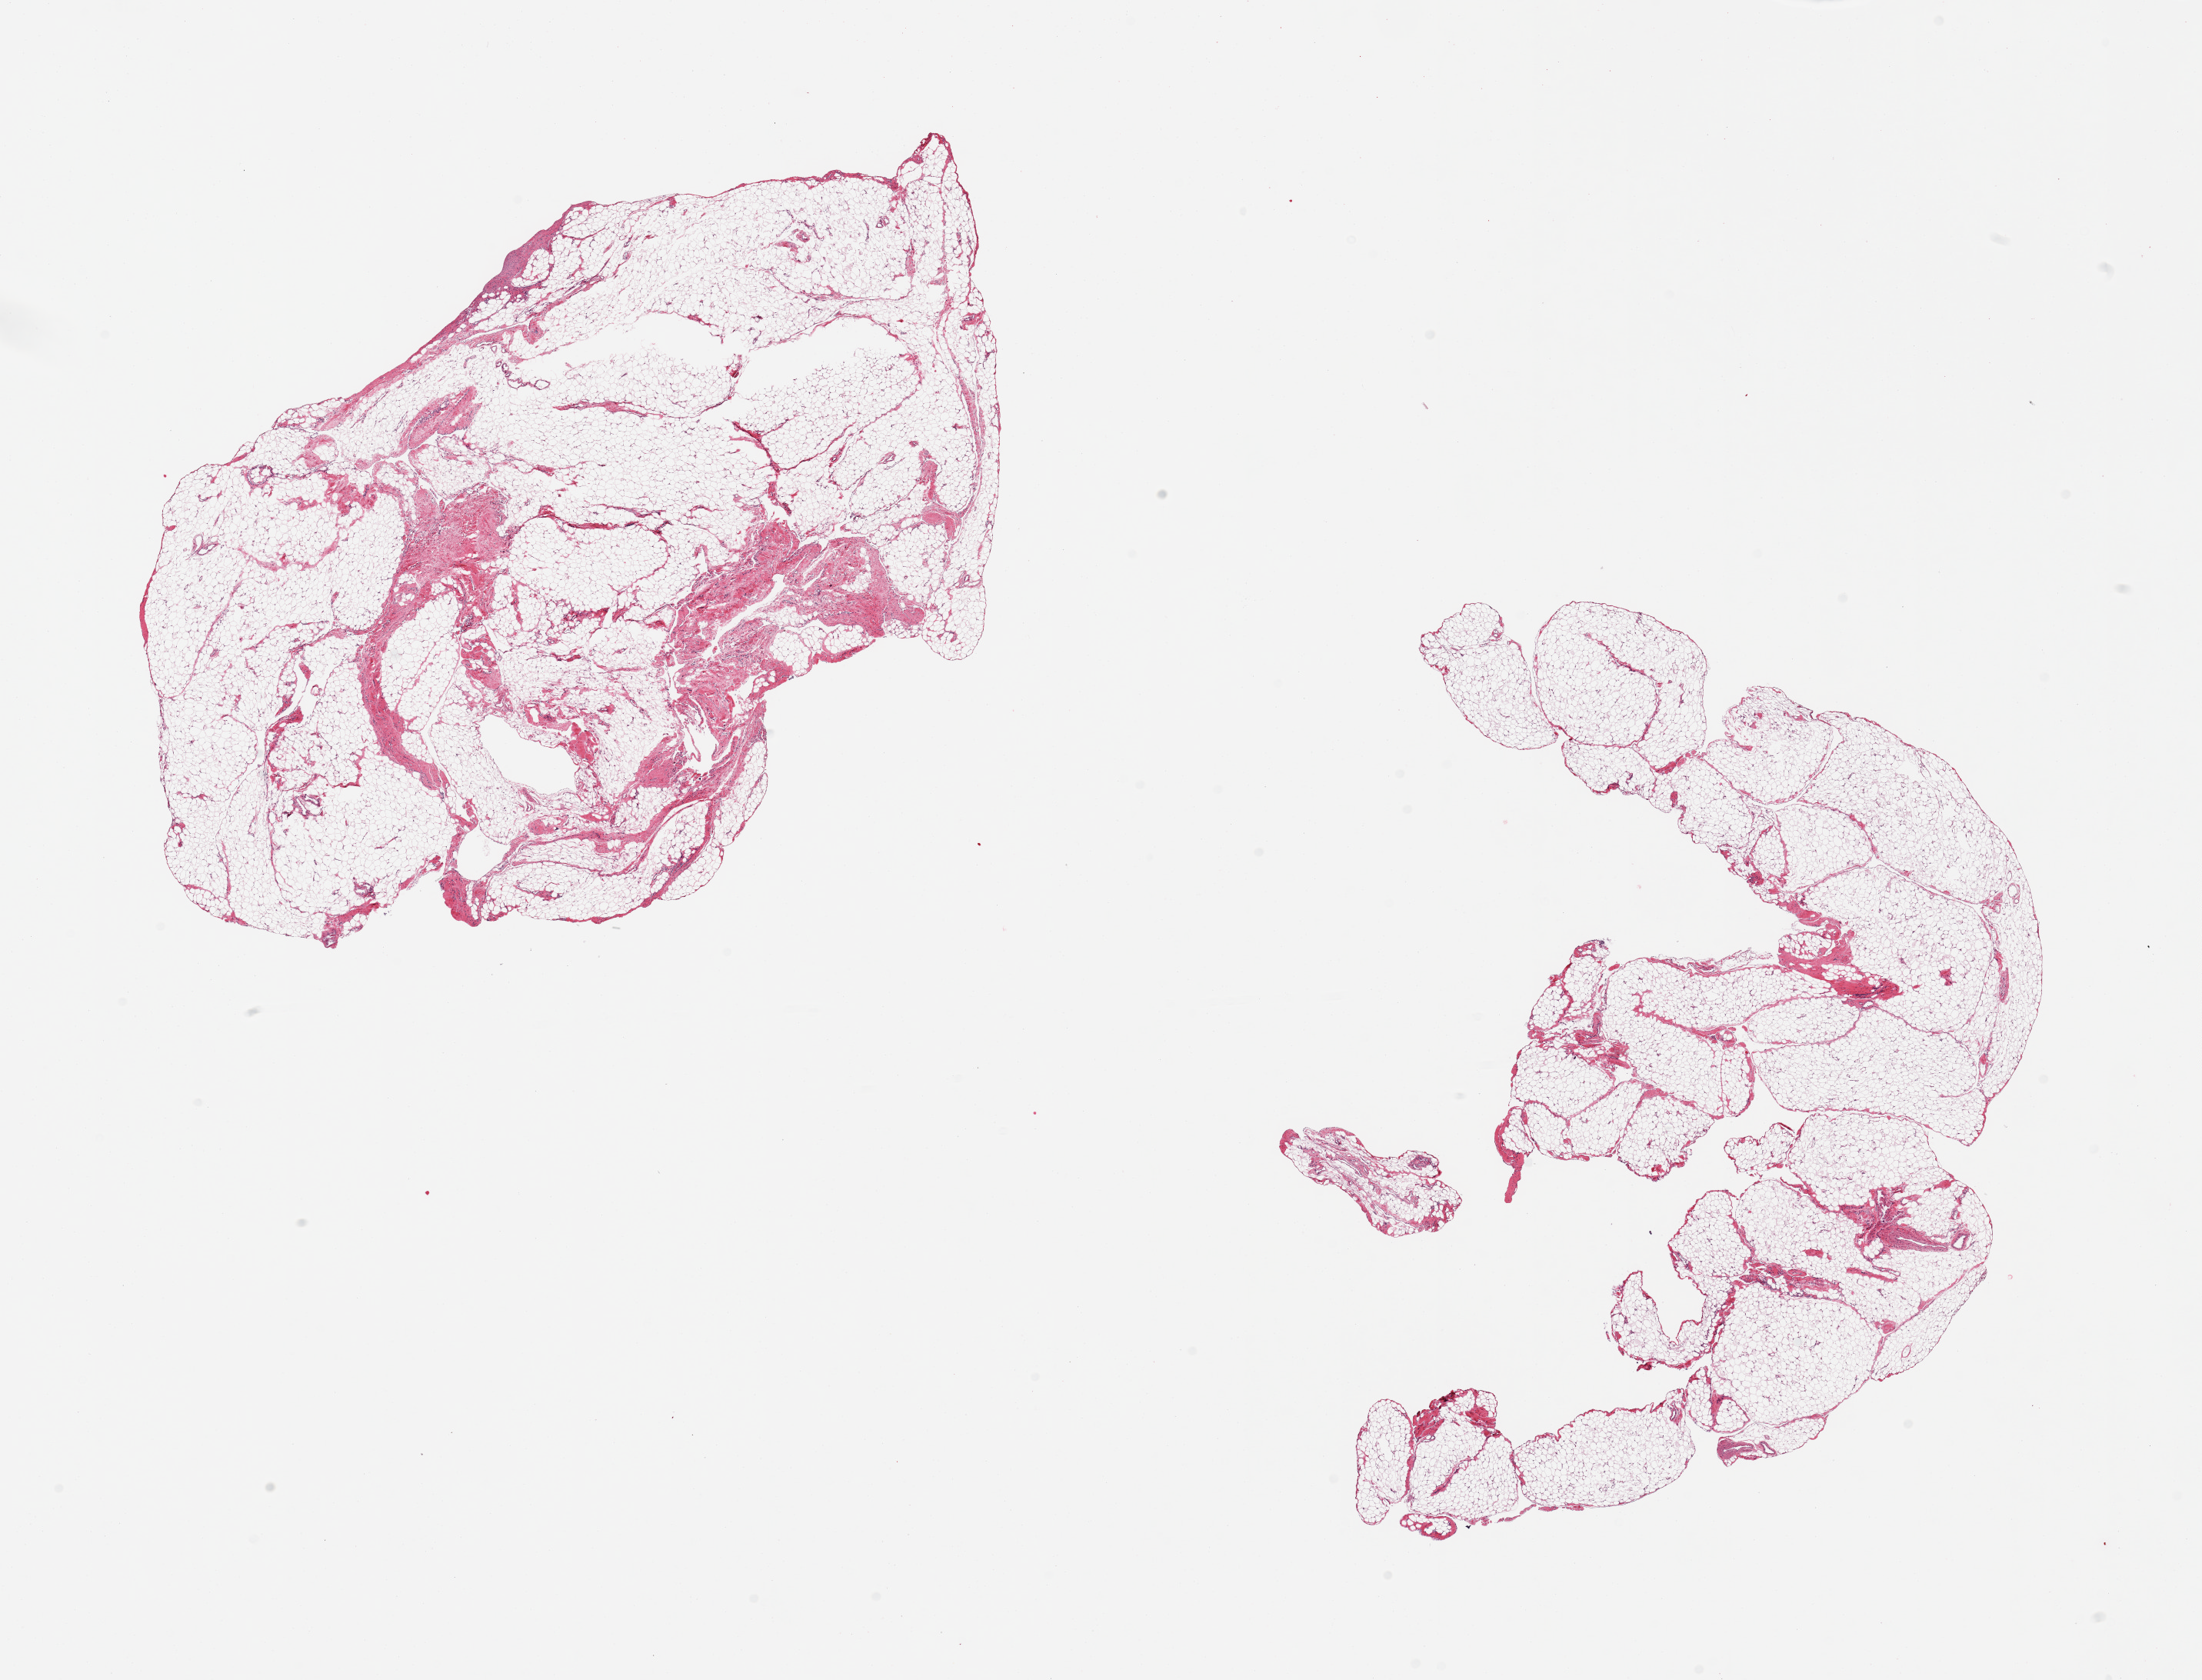
Digitized H&E-stained section, a low-resolution overview of the entire scanned area, about 22.6 x 17.3 mm (from a 20x scan), PAXgene-fixed paraffin-embedded (PFPE) section, target tissue: omentum, tissue donor sample. Donor sex: female.
Pathologist's review note for this sample: 2 pieces; 10% & <5% fibrous content.